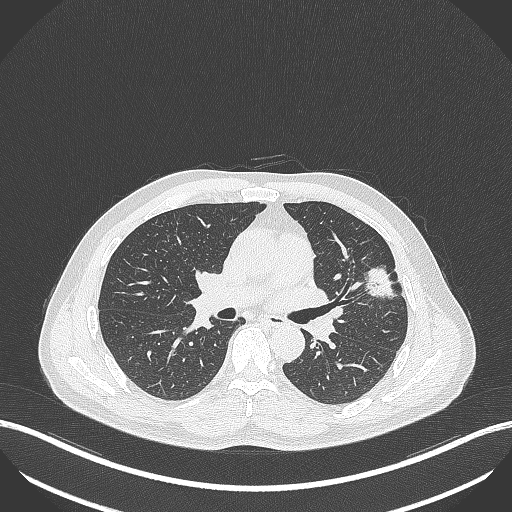
Chest CT, one axial slice. Position 224 of 418 along the scan axis. Reconstruction kernel B70f. Lung window (W 1500 / L -600 HU). 1 mm slice thickness. 512 × 512 image matrix, field of view 400 × 400 mm. Patient: male, 55 years. From the clinical record (not read from this slice): clinical TNM (as recorded): T1c N0 M0; histopathological grade: G2-3.
Structures marked on this image (rectangle marked by the reading radiologist):
- lung tumour (recorded histology: adenocarcinoma): bounding box <362,261,399,301> (left, top, right, bottom; pixels)